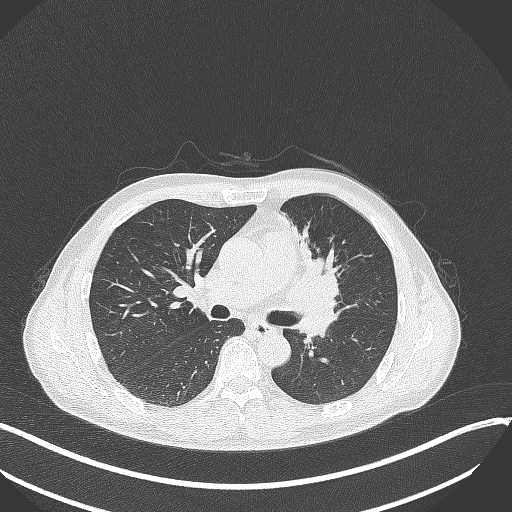
Chest CT, one axial slice. Slice 196 of 411 in the series (ordered by position). Reconstruction kernel B70f. 120 kVp. Lung window (W 1500 / L -600 HU). 1 mm slice thickness. 512 × 512 image matrix, field of view 400 × 400 mm. Patient: male, 56 years. Case-level facts recorded for this patient, not image findings: clinical TNM (as recorded): T2a N0 M0.
Annotated regions visible in this slice (bounding box drawn by a radiologist):
- lung tumour (recorded histology: squamous cell carcinoma): box from (x=273, y=260) to (x=344, y=318) px